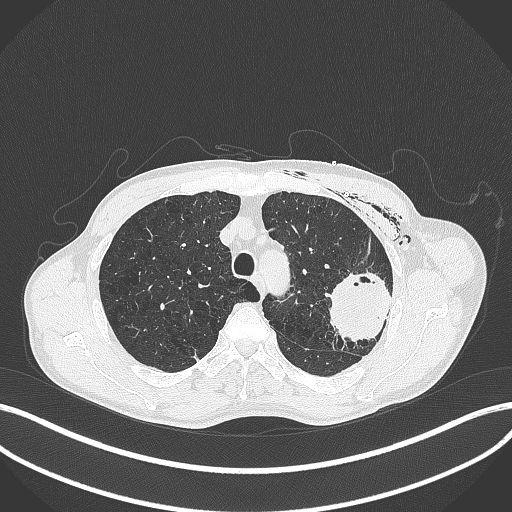
Chest CT, one axial slice. 120 kVp. Lung window (W 1500 / L -600 HU). 1 mm slice thickness. 512 × 512 image matrix, field of view 400 × 400 mm. Patient: male, 58 years. From the clinical record (not read from this slice): clinical TNM (as recorded): T3 N0 M0.
Annotated regions visible in this slice (bounding box drawn by a radiologist):
- lung tumour (recorded histology: adenocarcinoma): box from (x=325, y=267) to (x=395, y=346) px